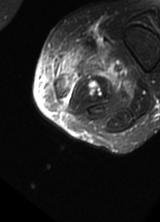
MRI of an extremity soft-tissue mass, one axial slice; slice 9 of 69 in the series (ordered by position); T2-weighted fat-saturated; MR volume resampled by the dataset authors to the PET/CT grid (not the native acquisition matrix); 160 × 222 image matrix, field of view 156 × 217 mm. Female patient. From the clinical record (not read from this slice): histological type: pleomorphic leiomyosarcoma; grade: high; site of the primary tumour: left thigh.
Structures marked on this image (expert contour drawn on MRI and transferred to this co-registered scan by the dataset authors):
- gross tumour volume including surrounding oedema: bounding box <54,36,135,103> (left, top, right, bottom; pixels)